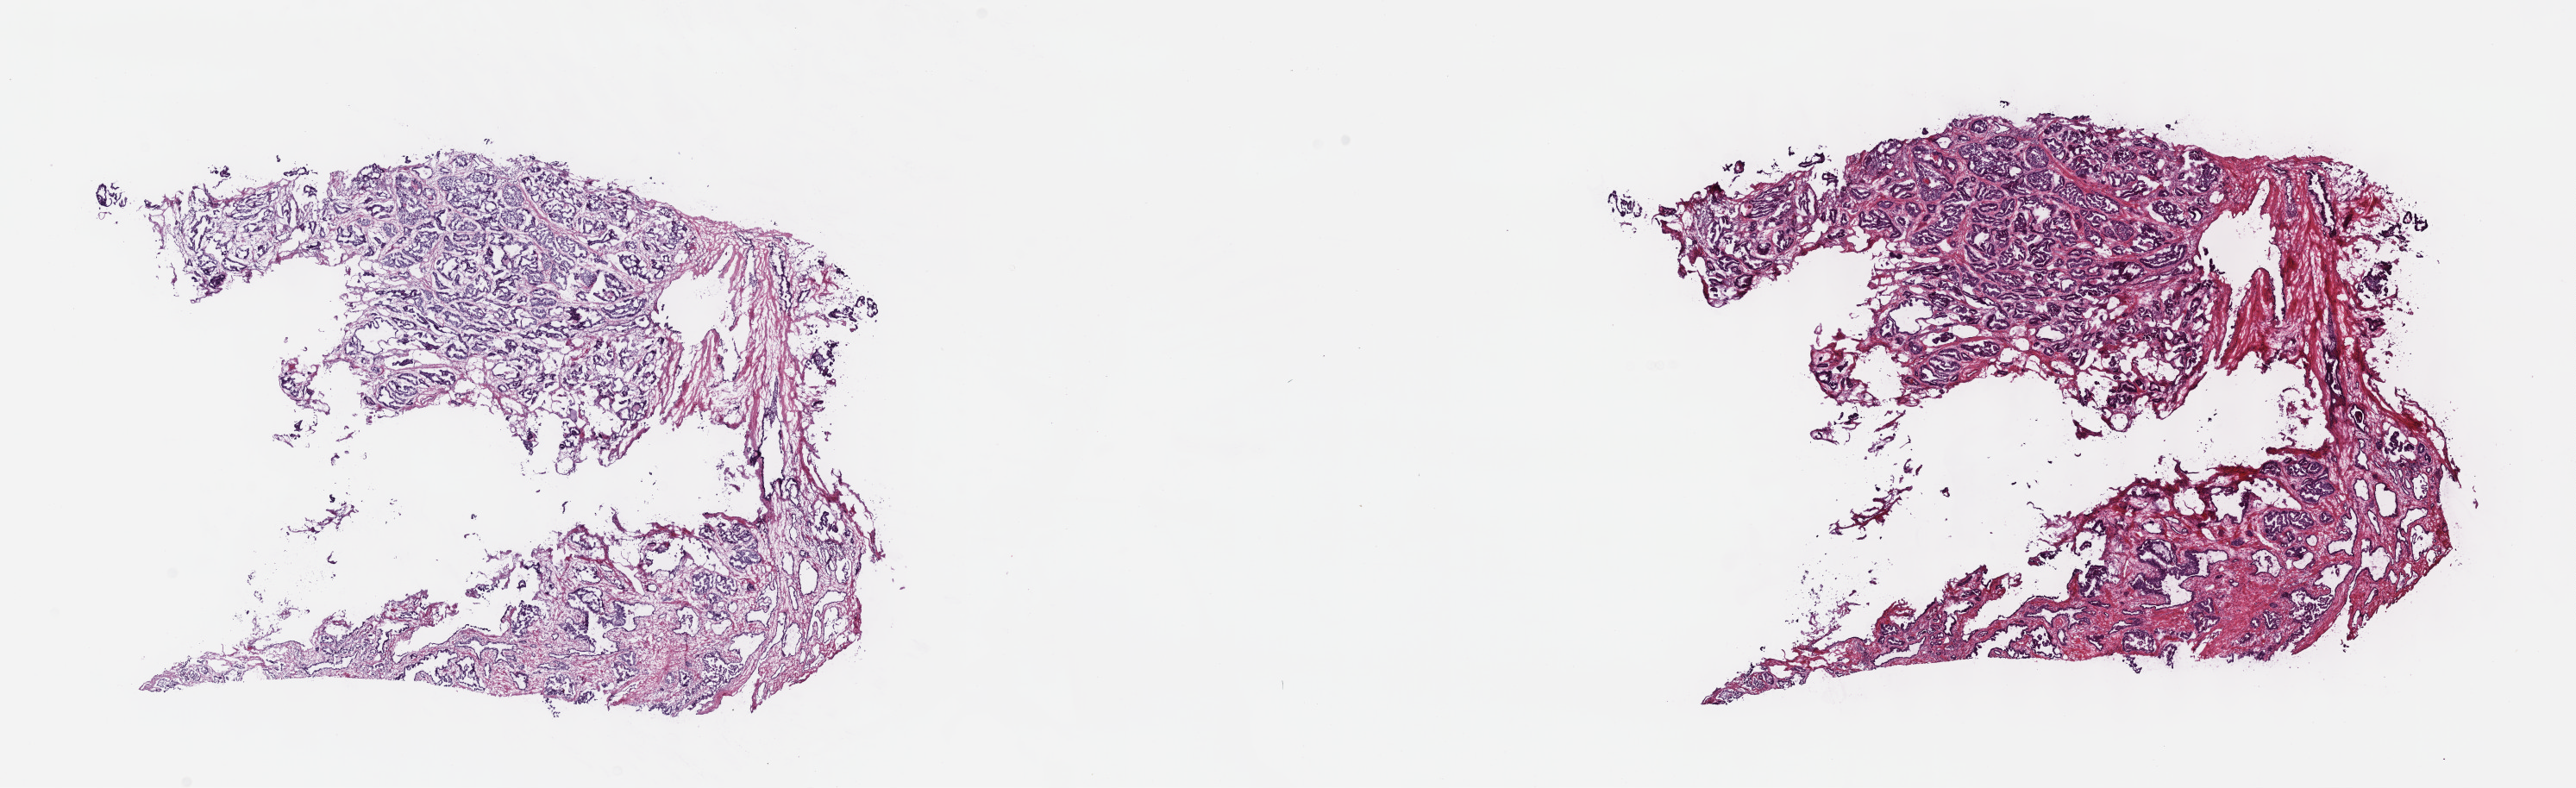
Digitized Hematoxylin and eosin (H&E) stained tissue section (whole slide) — a low-resolution overview of the entire scanned area, about 24.2 x 7.4 mm, frozen section from the top of the tissue portion, primary tumour sample from the prostate. Patient: male, age at initial diagnosis 60 years. Gleason score: 8 (4+4). Pathologist review of this section (percent, as recorded): tumour cells 70%, tumour nuclei 80%, normal cells 0%, stromal cells 30%, necrosis 0%. Inflammatory infiltration, as recorded: lymphocyte infiltration 0%, monocyte infiltration 0%, neutrophil infiltration 0%.
Histologic diagnosis: Adenocarcinoma, NOS (prostate gland). Laterality: bilateral.